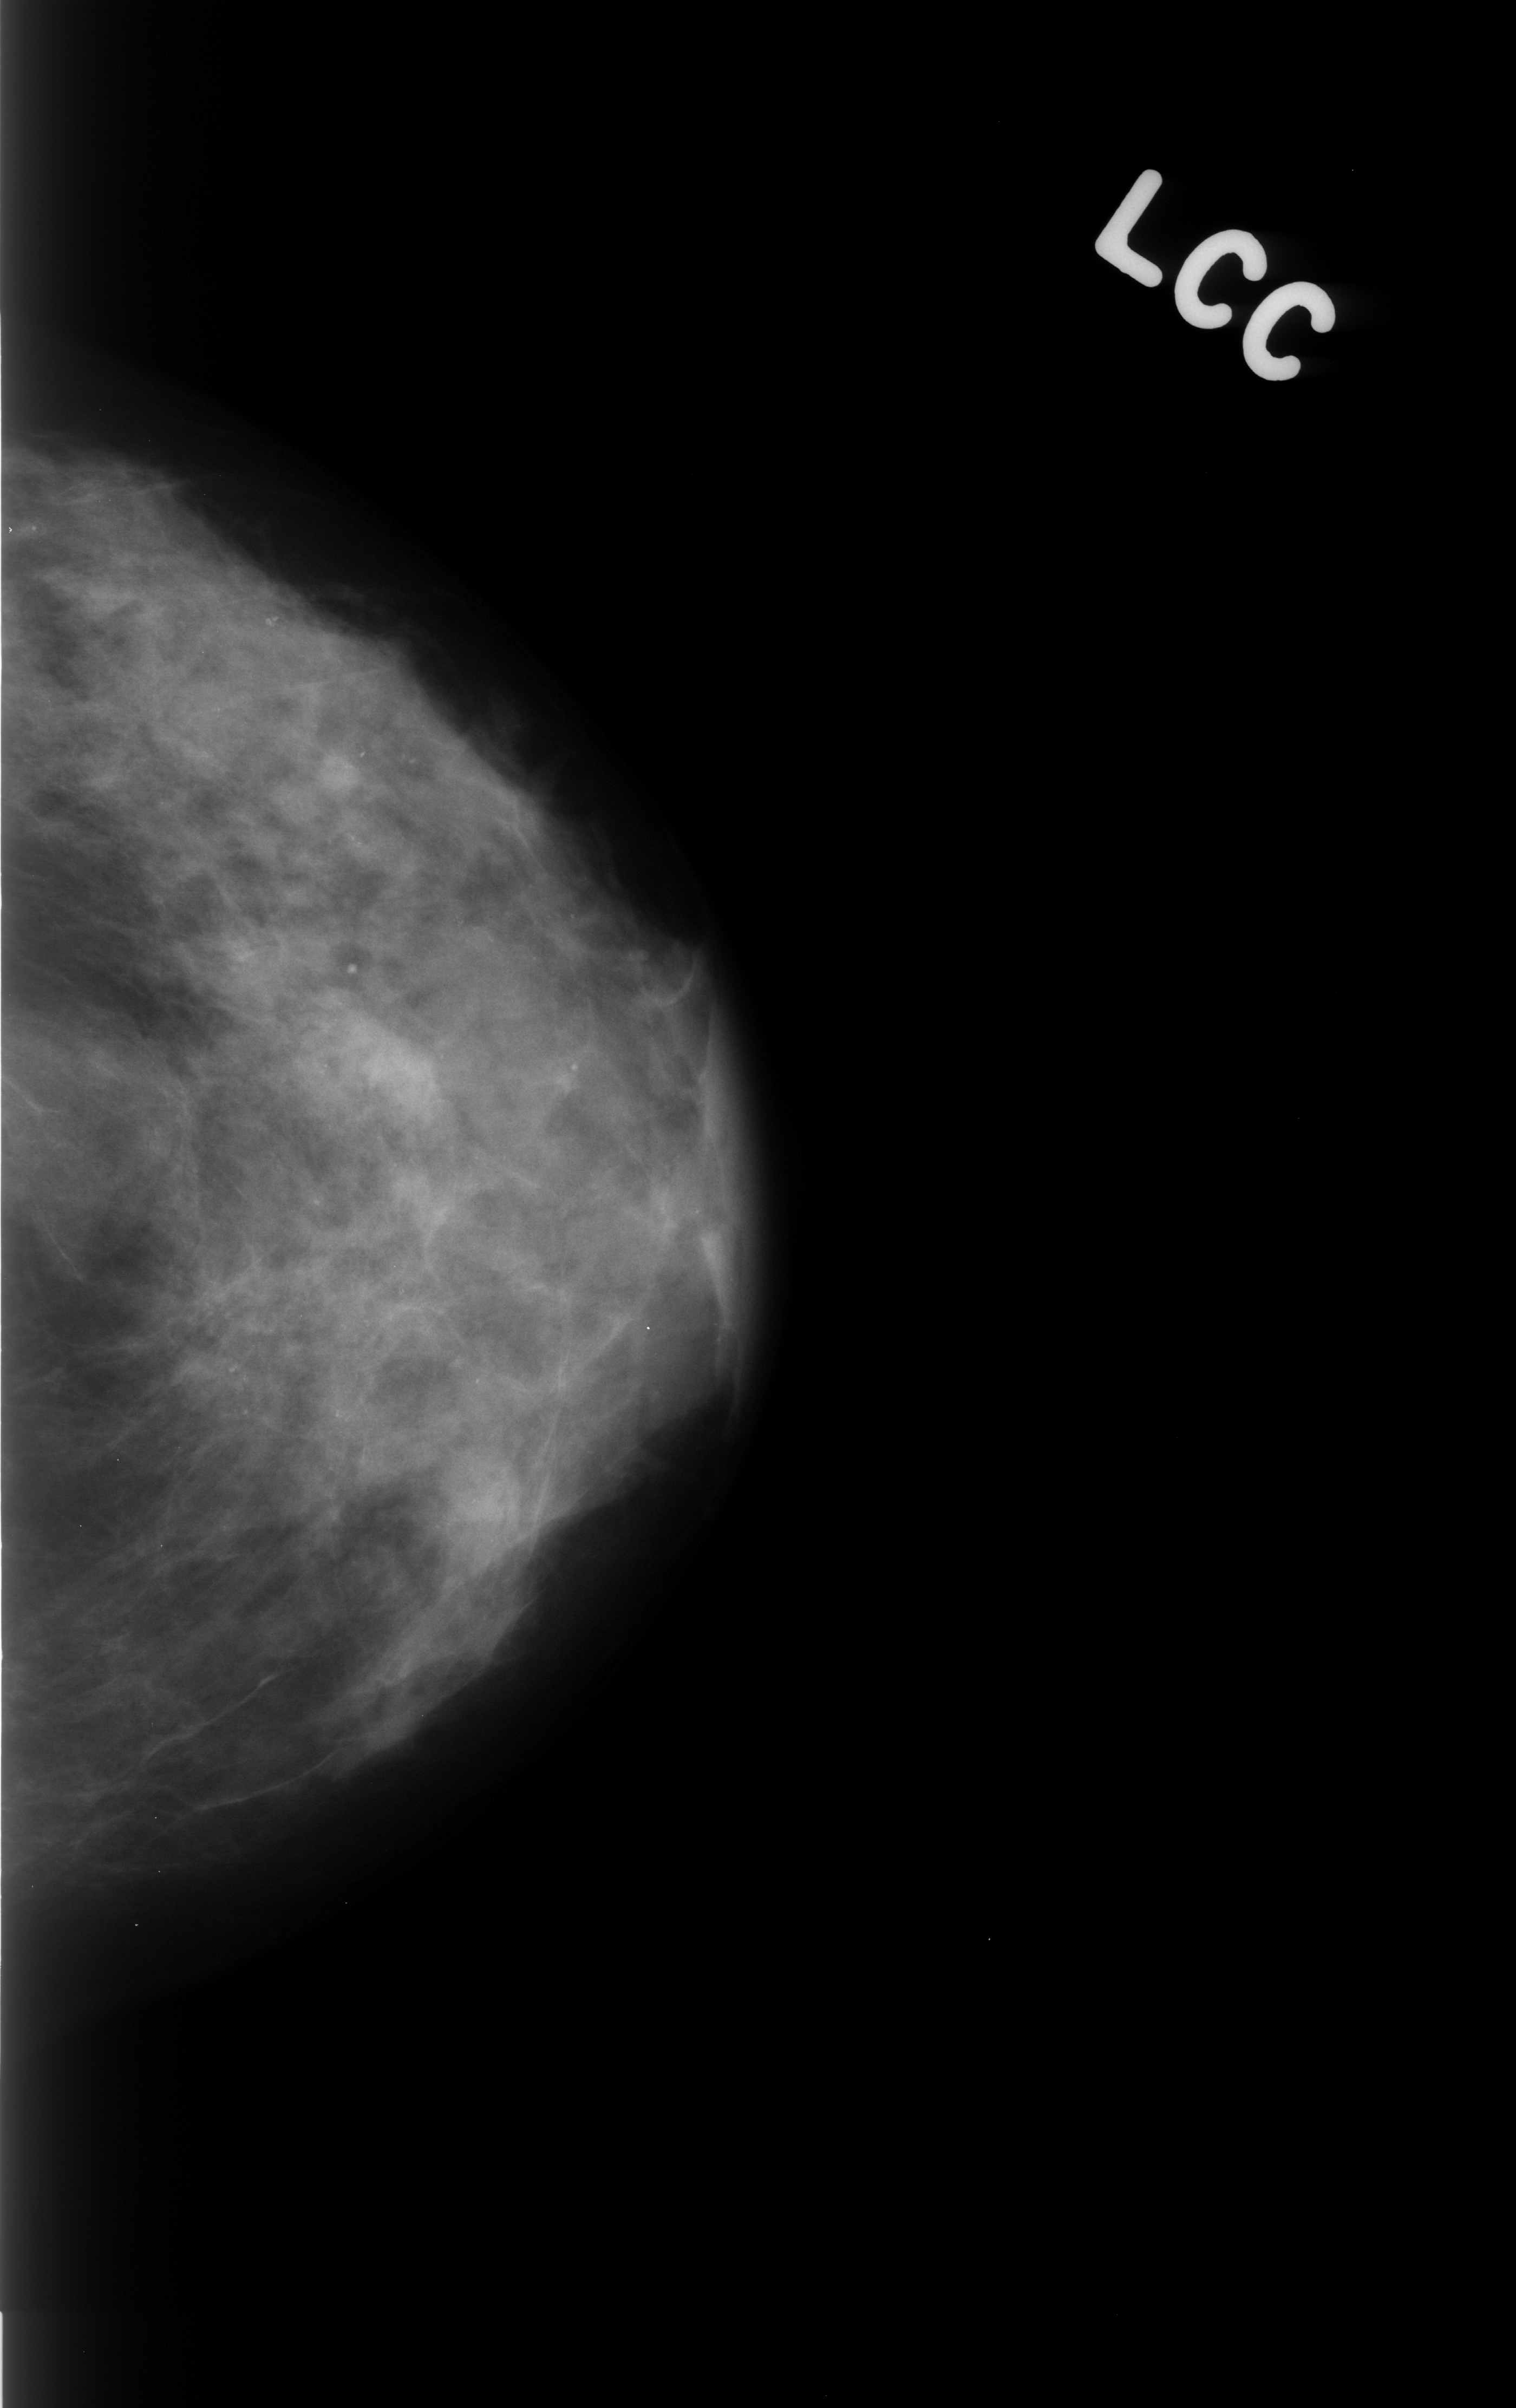
Digitized screen-film mammogram; left breast; CC view; breast composition: heterogeneously dense (BI-RADS density category 3 of 4).
- Finding: calcifications, morphology pleomorphic, distribution diffusely scattered; BI-RADS assessment category 3; pathology (as recorded): benign.